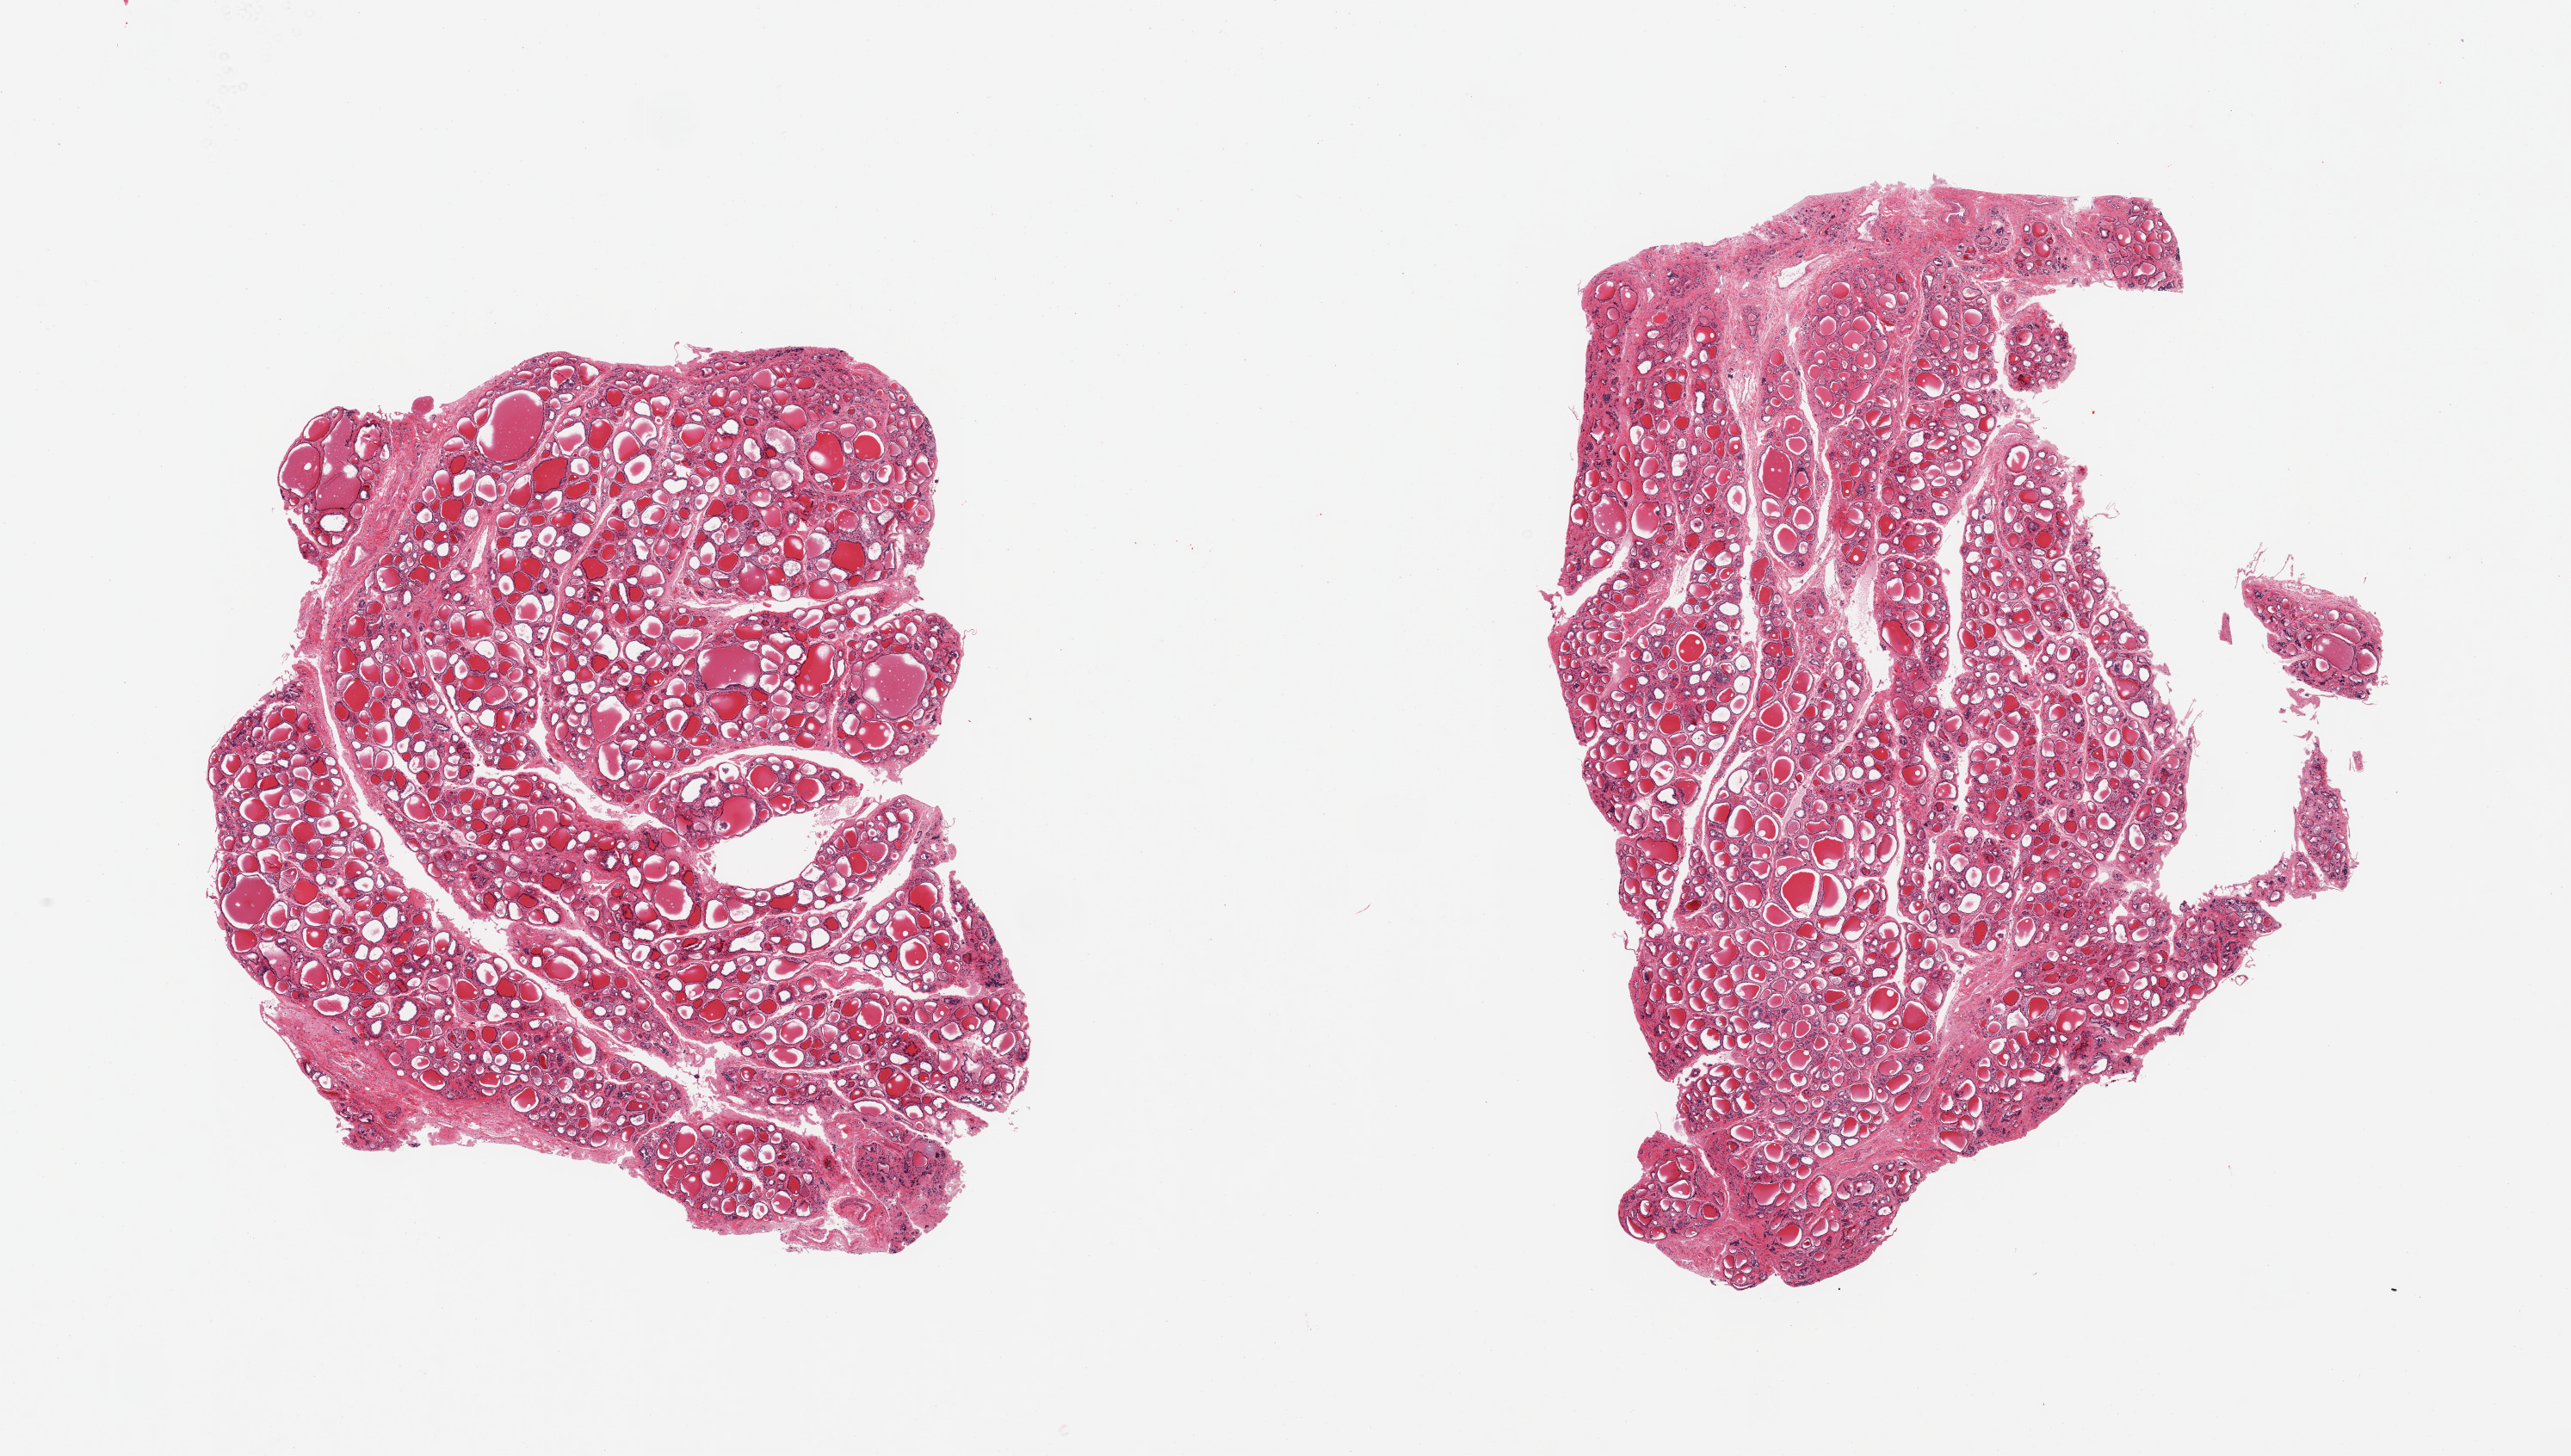
Digitized haematoxylin and eosin-stained section, brightfield, shown as a low-resolution overview of the whole scanned area (about 23.6 x 13.4 mm, slide scanned at 20x), PAXgene-fixed, paraffin-embedded tissue, sampled site (target tissue): thyroid, tissue donor sample. Donor: male.
Pathologist's review note for this sample: 2 pieces.